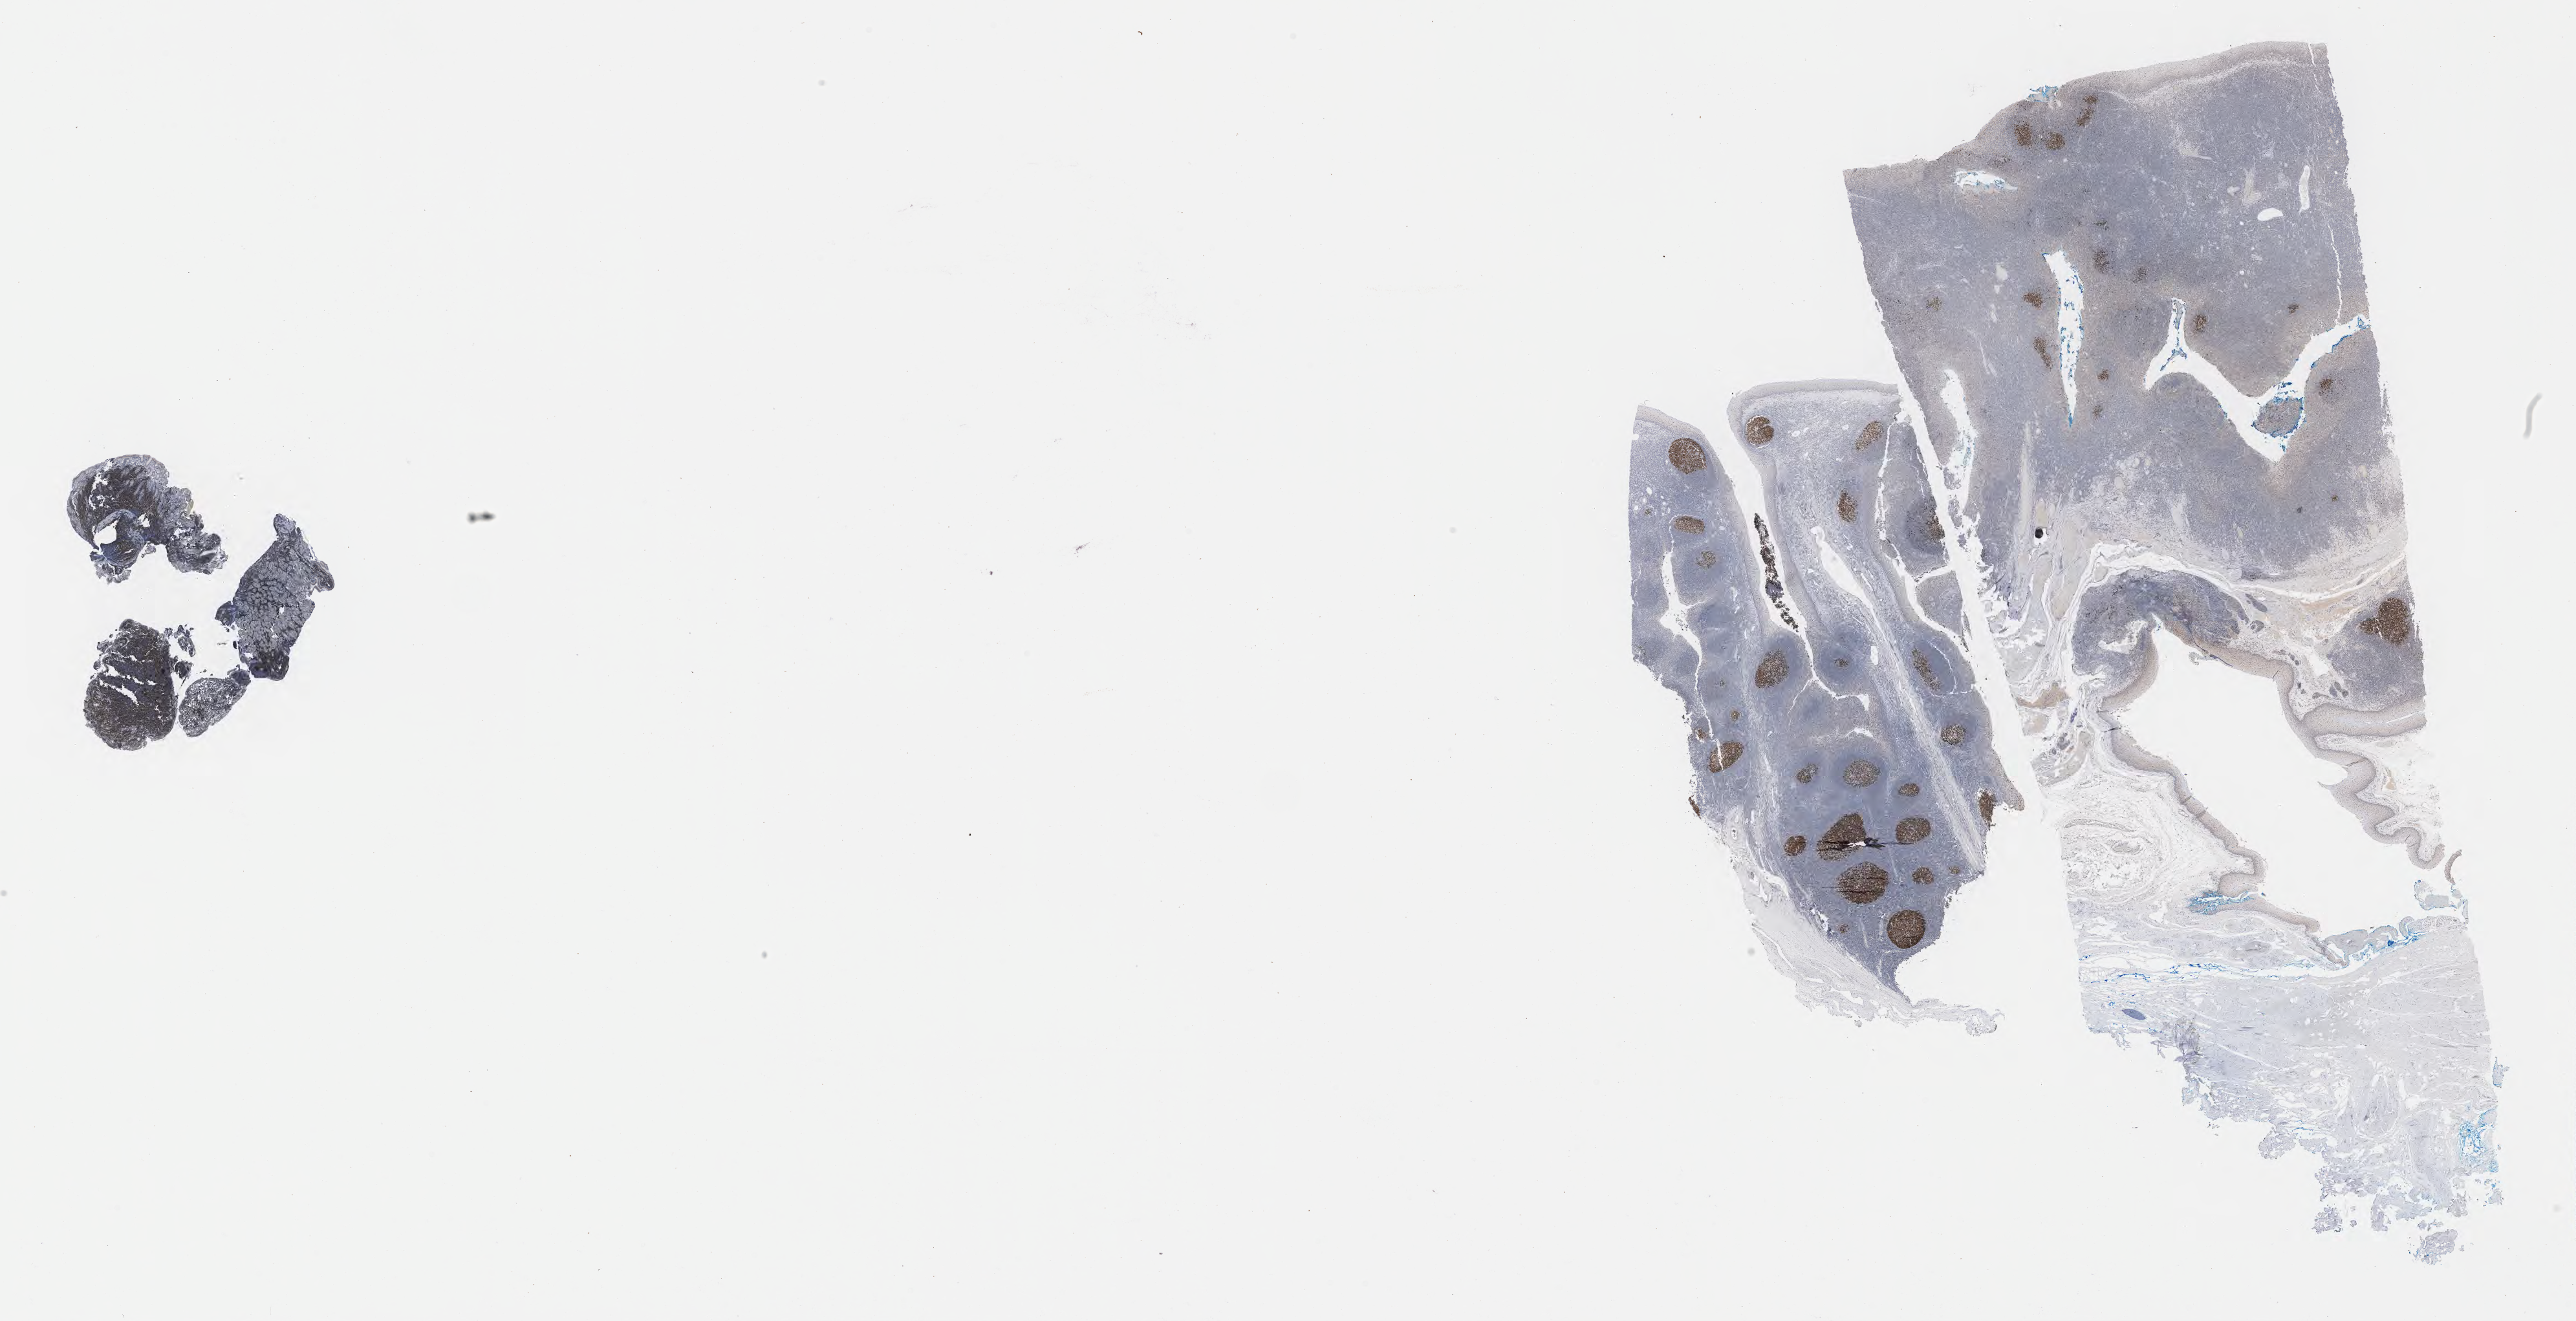
IHC for BCL6, whole-slide image — low-resolution overview of the scanned area, about 32.2 x 16.5 mm. Specimen: tumor tissue. Female patient, 45 years old.
Histologic diagnosis: Burkitt lymphoma, NOS.